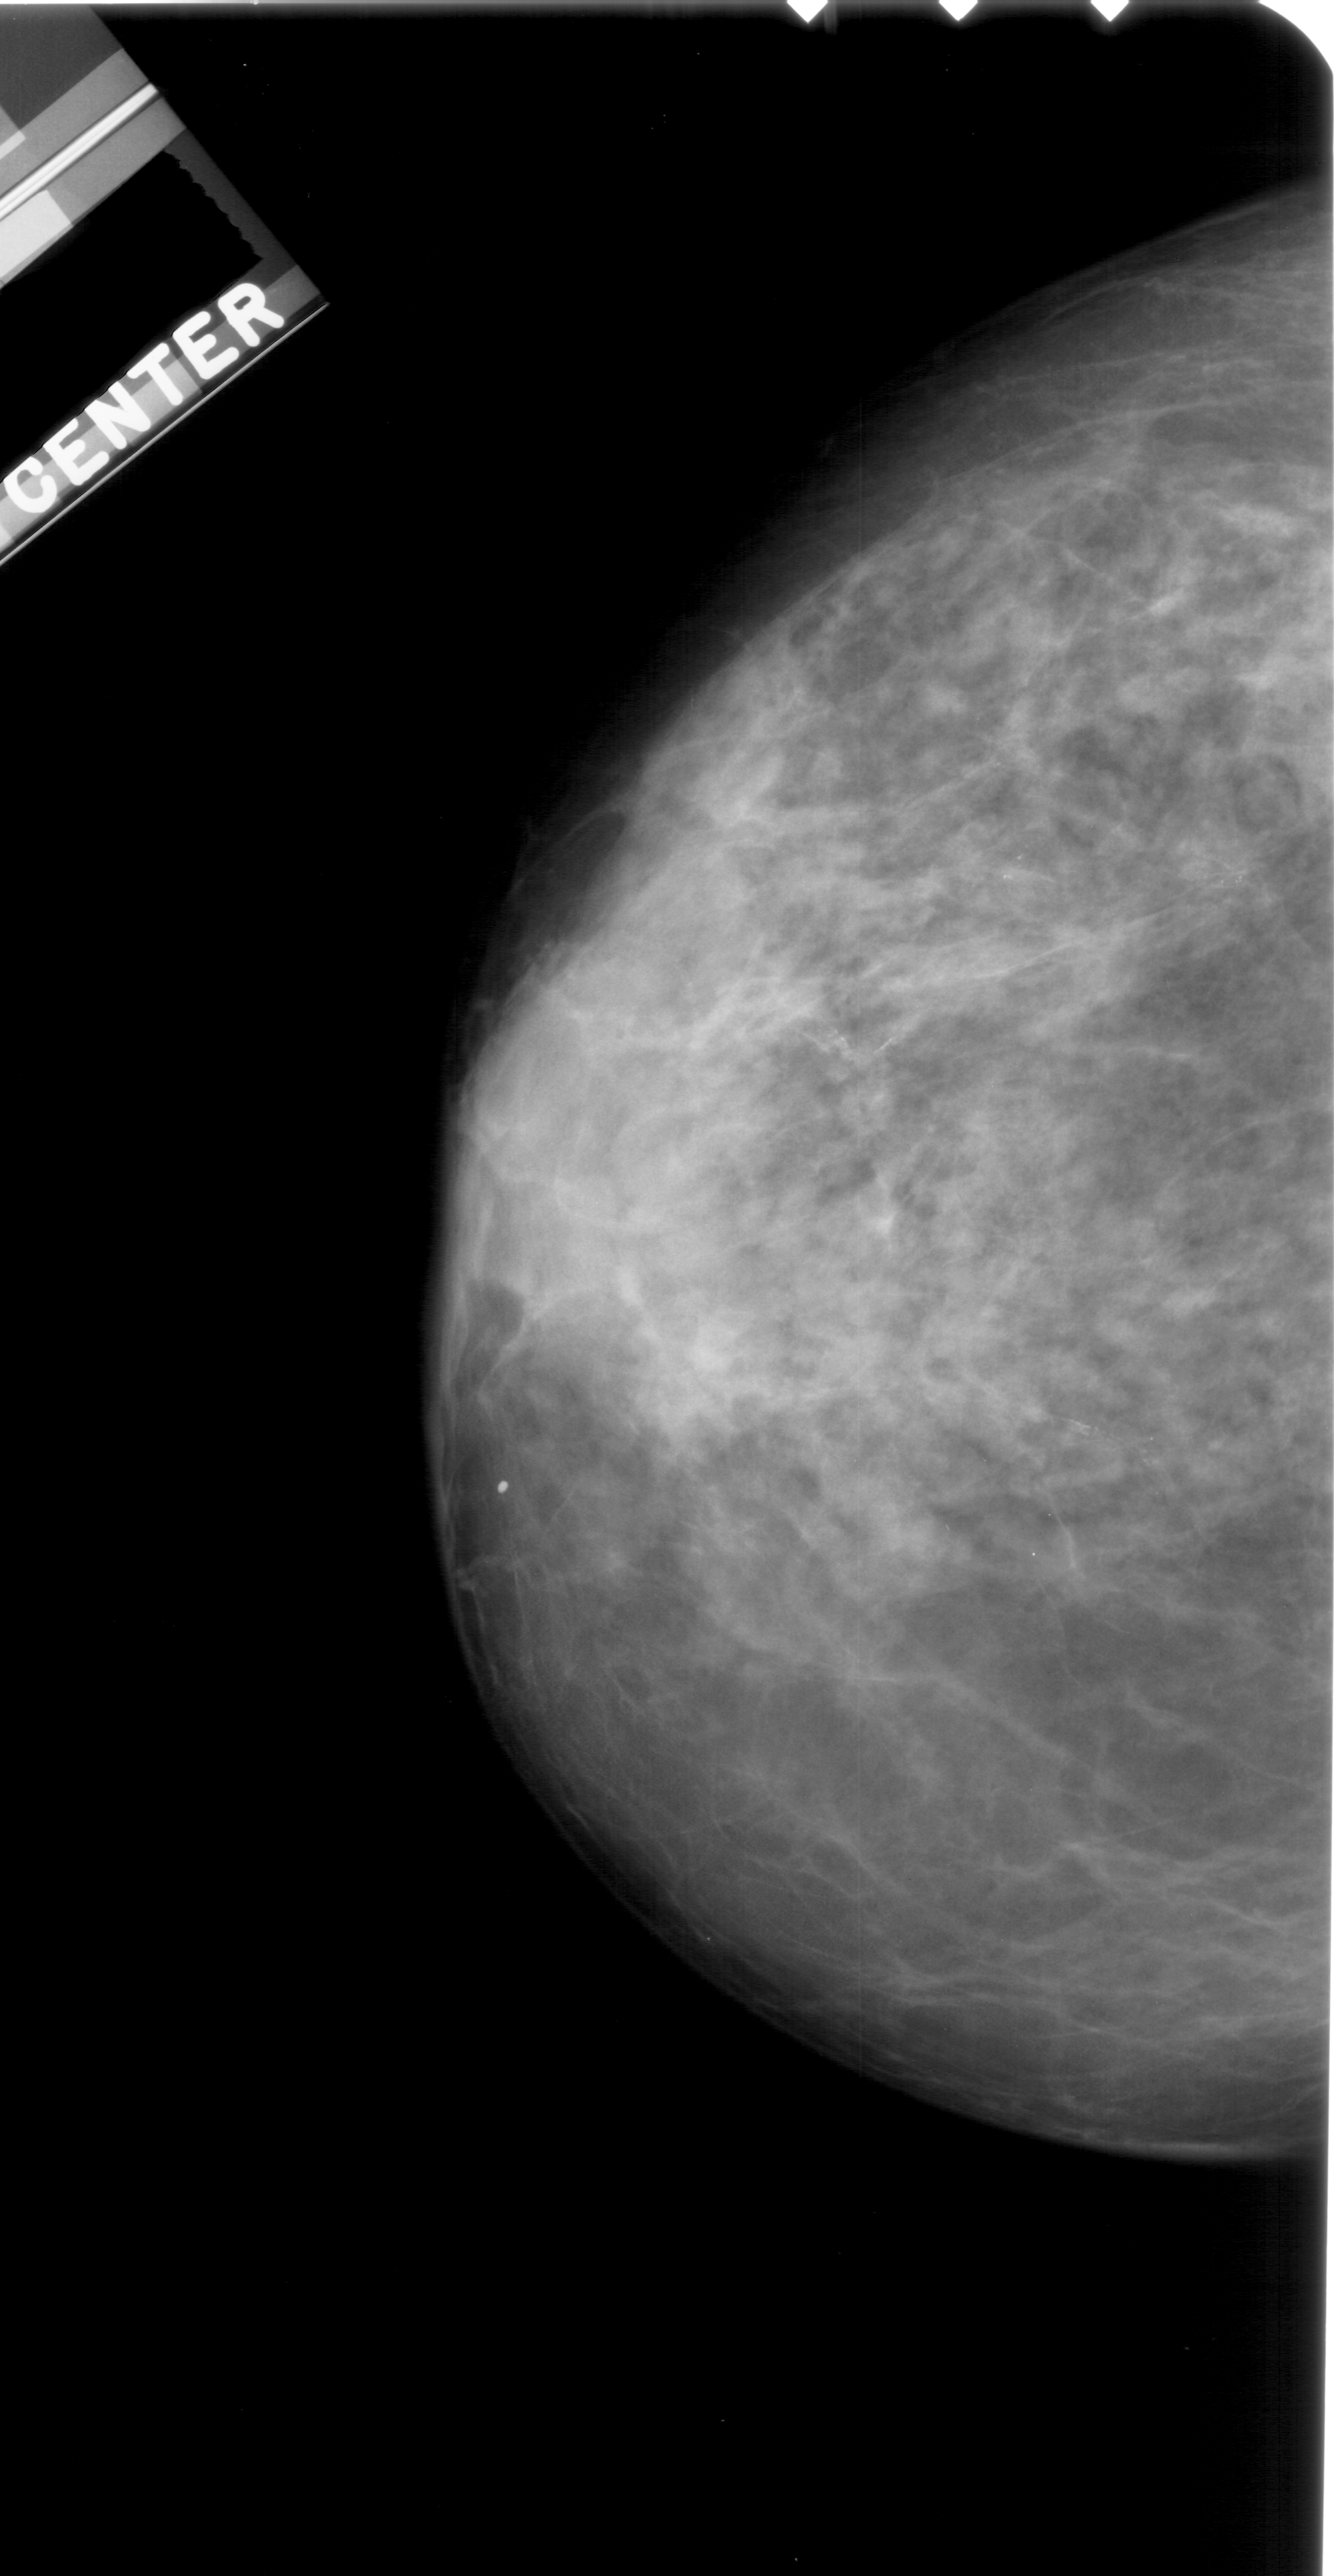
Mammogram (digitized film); left breast; craniocaudal (CC) view; BI-RADS breast density category 3 (scale 1–4); 1334 × 2576 image matrix.
Marked abnormalities (boxes around the expert regions of interest):
- calcifications, morphology pleomorphic, distribution segmental; BI-RADS assessment category 4; pathology result (as recorded, not read from the image): malignant: bounding box <987,822,1273,926> (left, top, right, bottom; pixels)